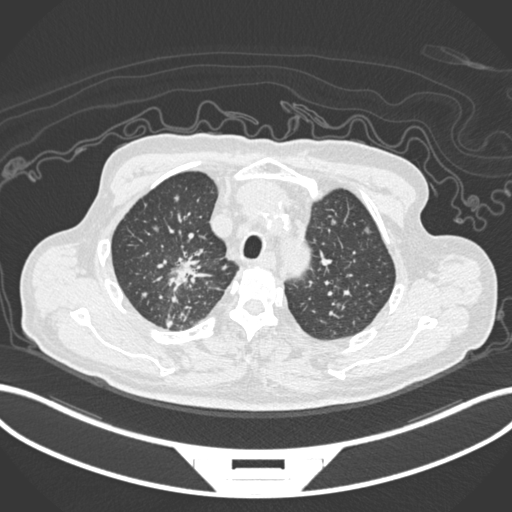
Chest CT, one axial slice; slice 170 of 207 in the series (ordered by position); lung window (W 1500 / L -600 HU); 1 mm slice thickness; 512 × 512 image matrix. Patient: male, 69 years. Case-level facts recorded for this patient, not image findings: clinical TNM (as recorded): T1c N1 M1.
Structures marked on this image (rectangle marked by the reading radiologist):
- lung tumour (recorded histology: adenocarcinoma): bounding box [x1, y1, x2, y2] px = [160, 243, 217, 296]